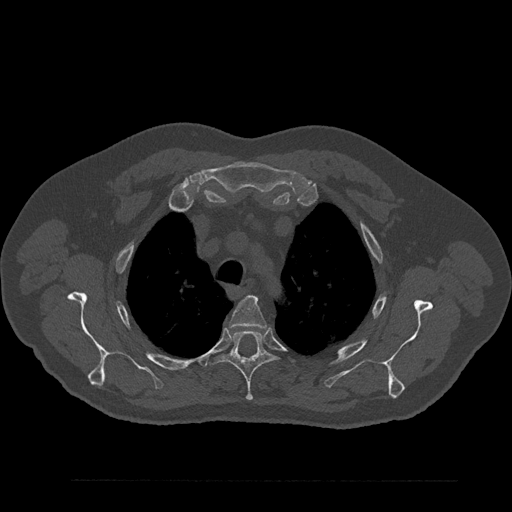
CT including the spine, one axial slice. Slice 653 of 797 in the series (ordered by position). 120 kVp. Bone window (W 1800 / L 400 HU). 512 × 512 image matrix, field of view 430 × 430 mm. Patient: male, 61 years. From the clinical record (not read from this slice): primary cancer: prostate.
Structures marked on this image (semi-automatic segmentation, software-assisted and operator-edited):
- T3 vertebra: bounding box <229,296,266,329> (left, top, right, bottom; pixels)
- T4 vertebra: <206,330,276,401>